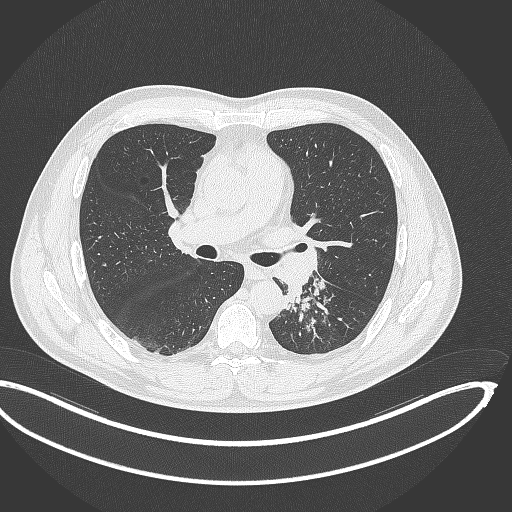
Chest CT, one axial slice. Position 207 of 362 along the scan axis. Reconstruction kernel B70f. 120 kVp. Lung window (W 1500 / L -600 HU). 512 × 512 image matrix, field of view 442 × 442 mm. Patient: male, 50 years. Case-level facts recorded for this patient, not image findings: clinical TNM (as recorded): T2a N3 M0.
Outlined on this slice (bounding box drawn by a radiologist):
- lung tumour (recorded histology: squamous cell carcinoma): box from (x=279, y=281) to (x=304, y=311) px